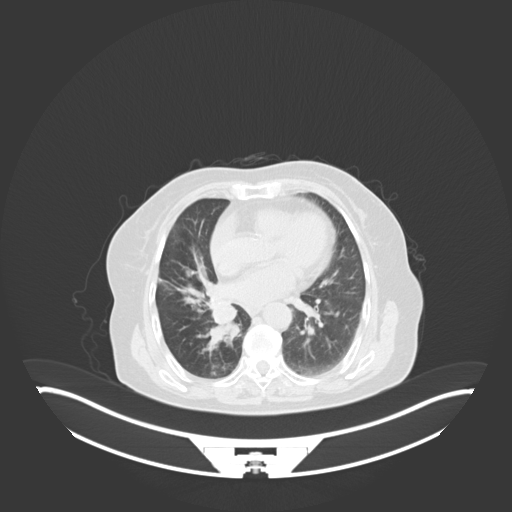
Chest CT, one axial slice. Position 23 of 76 along the scan axis. Reconstruction kernel B30f. 120 kVp. Lung window (W 1500 / L -600 HU). 3 mm slice thickness. 512 × 512 image matrix, field of view 500 × 500 mm. Patient: female, 75 years. From the clinical record (not read from this slice): clinical TNM (as recorded): T1b N0 M1a; histopathological grade: G1.
Annotated regions visible in this slice (bounding box drawn by a radiologist):
- lung tumour (recorded histology: squamous cell carcinoma): bounding box [x1, y1, x2, y2] px = [201, 295, 244, 348]